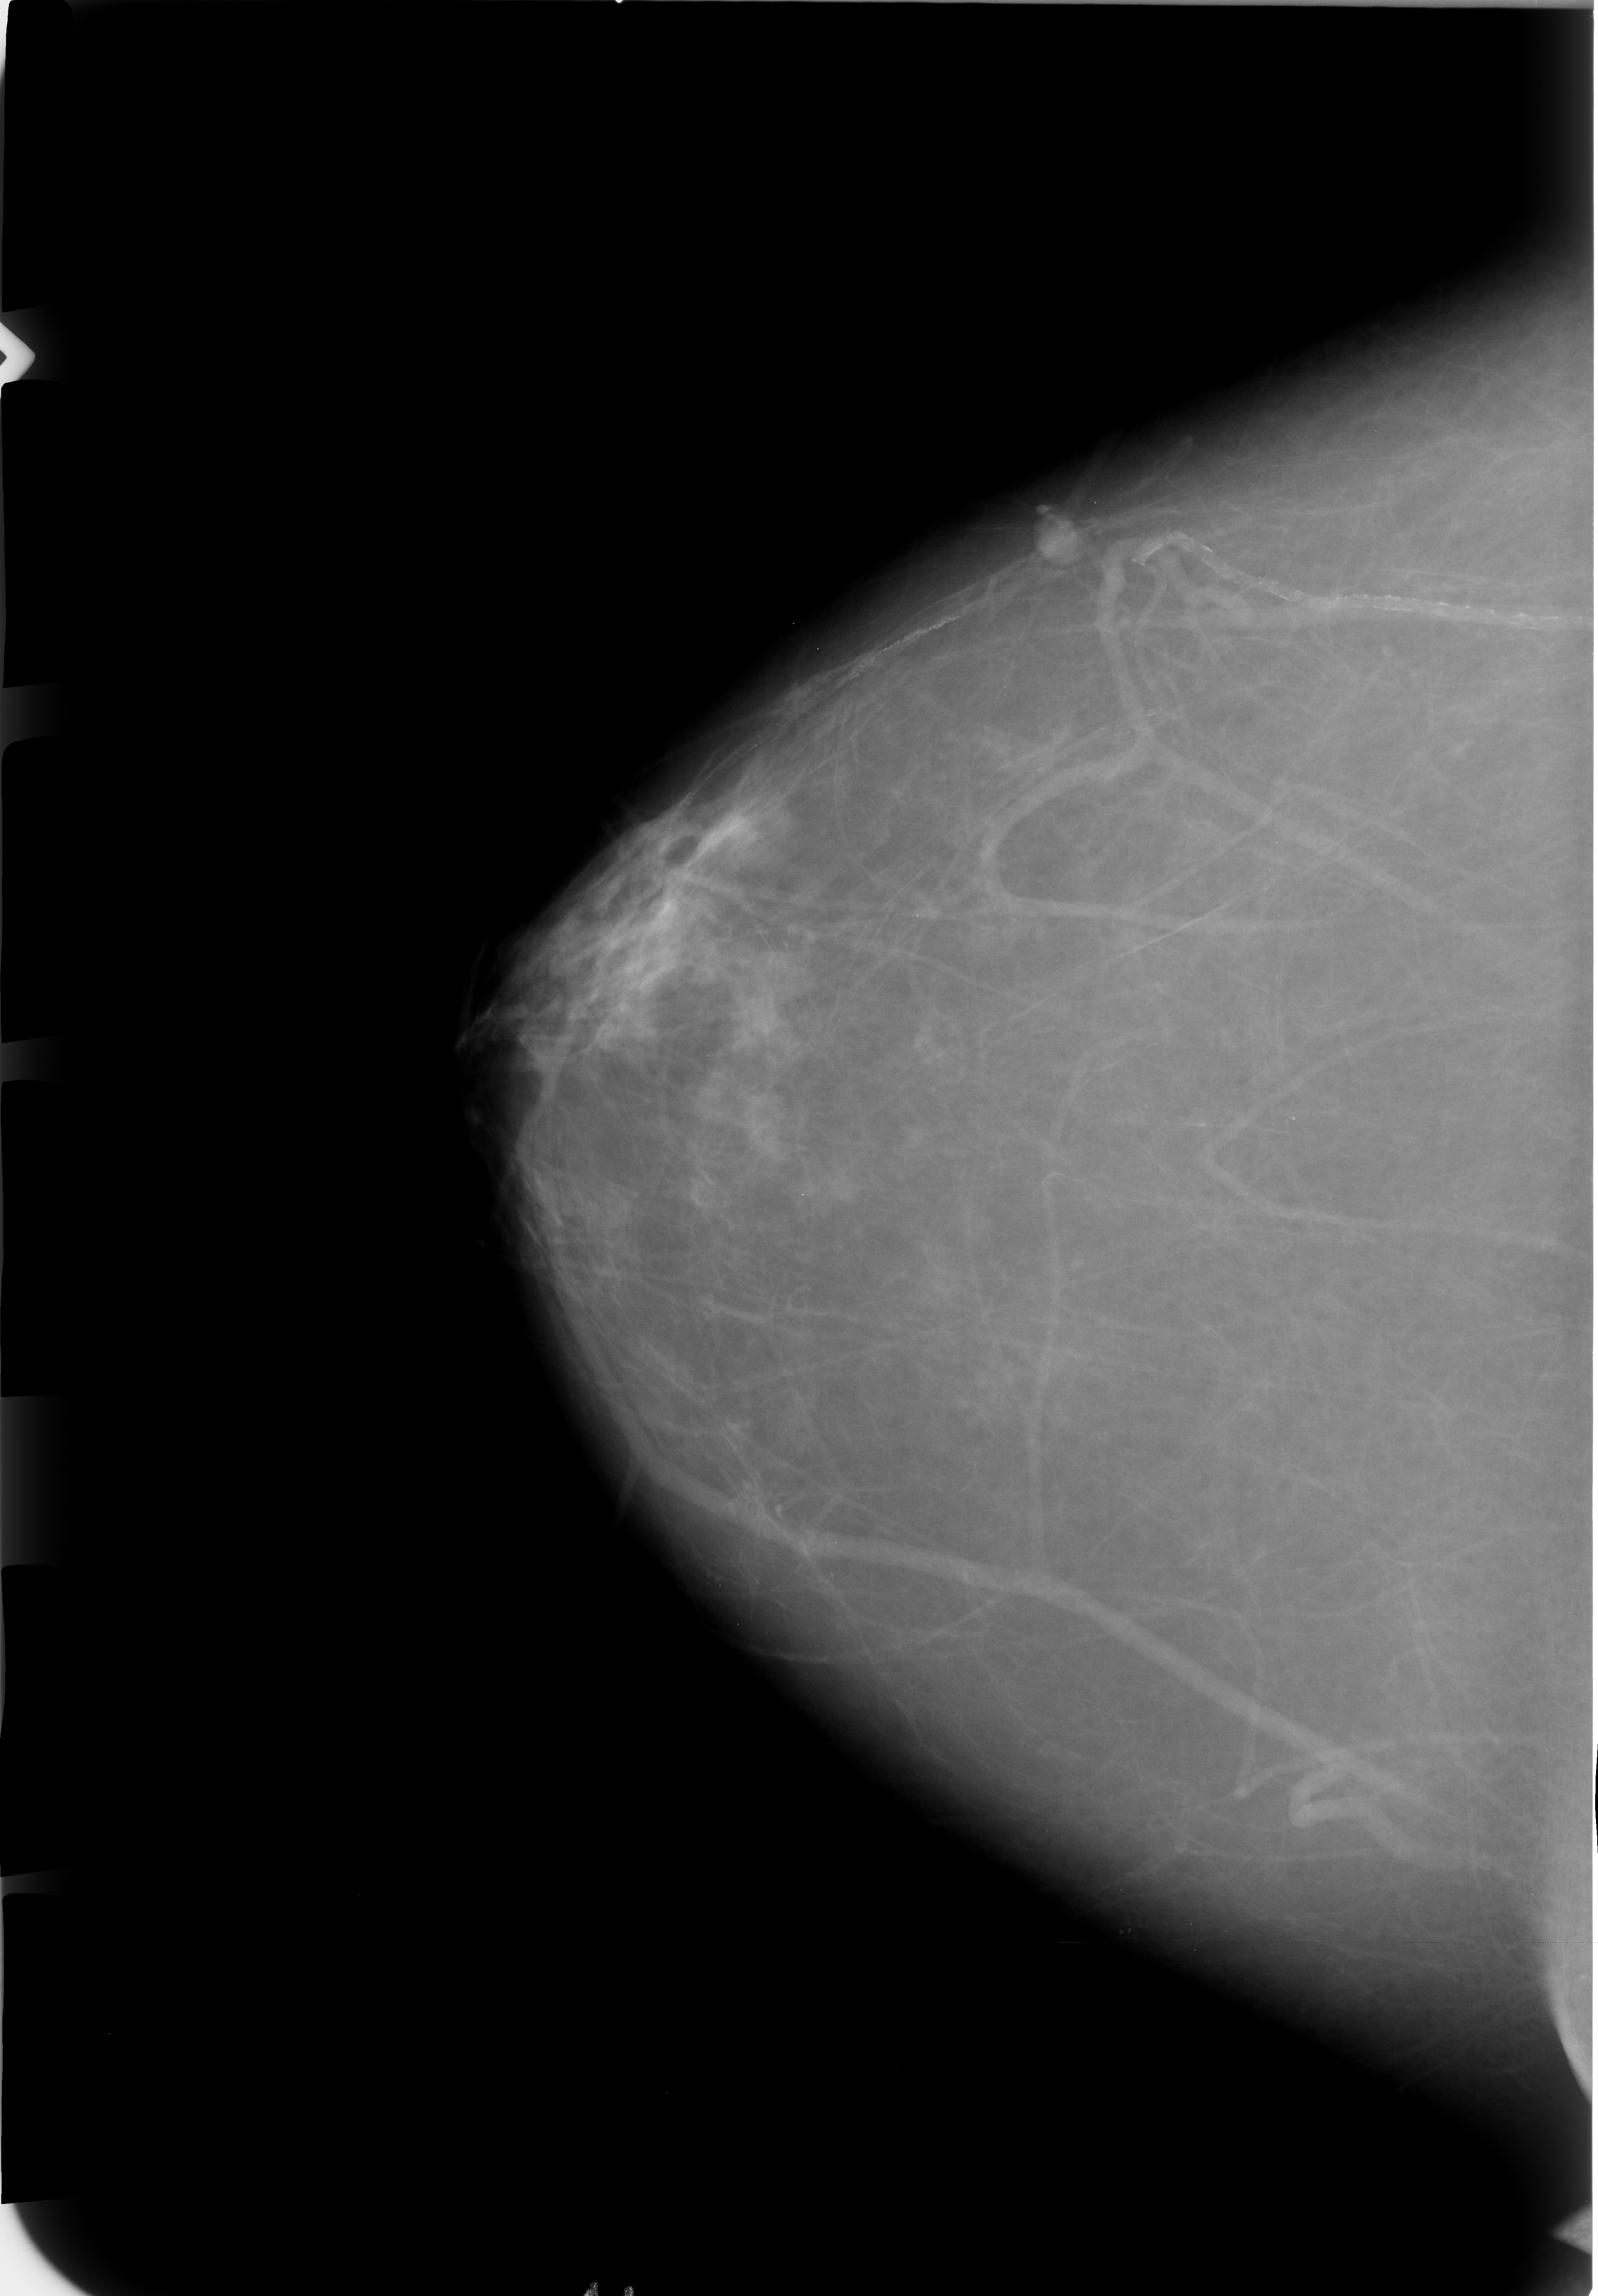
Mammogram (digitized film). Right breast. CC view. BI-RADS breast density category 2 (scale 1–4). 1598 × 2296 image matrix.
Marked abnormalities (boxes around the expert regions of interest):
- mass, shape oval / lymph node, margins circumscribed; BI-RADS assessment category 2; benign; no additional work-up was recommended (outcome (as recorded, no biopsy): benign without callback): box from (x=1027, y=498) to (x=1097, y=565) px